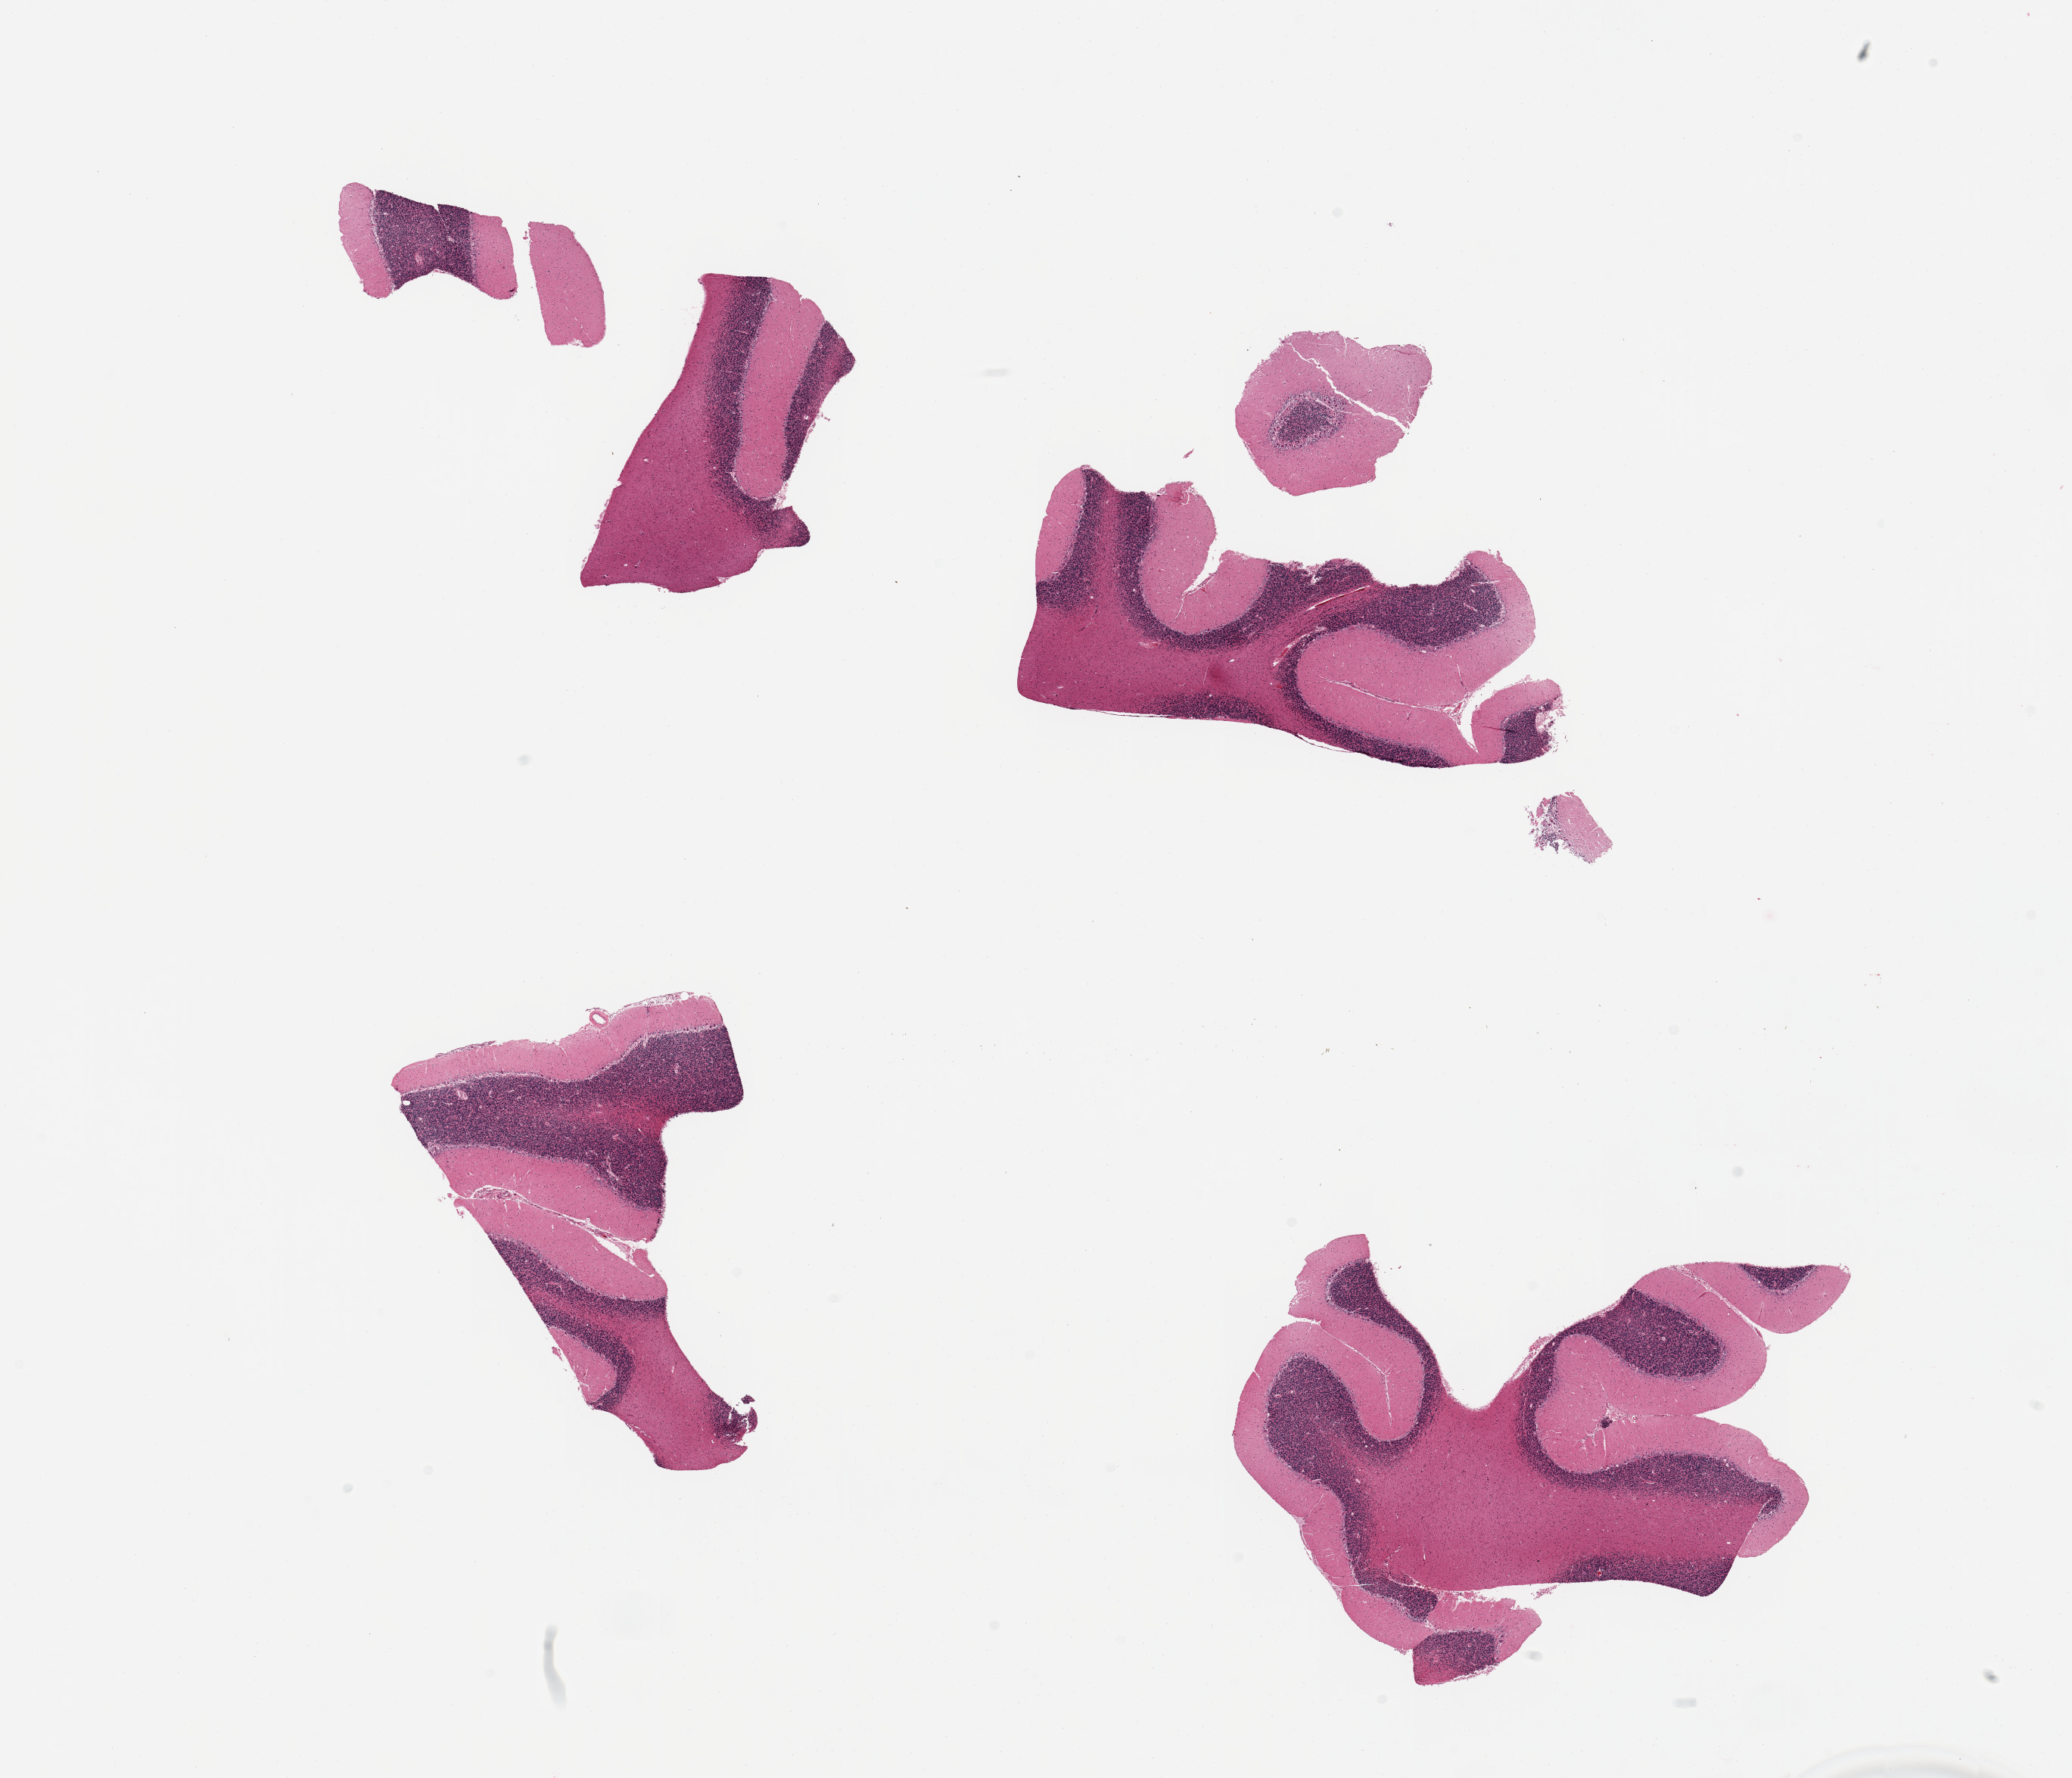
Whole-slide image, hematoxylin and eosin (H&E) stain, low-resolution overview of the scanned area, about 21.7 x 18.6 mm; PAXgene-fixed paraffin-embedded (PFPE) section; sampled site (target tissue): cerebellum; donor tissue sample.
Pathologist's review note for this sample: 4 pieces (fragmented); Purkinje cells well visualized, no evidence of hypoxic damage.